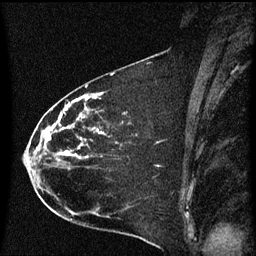
Breast MRI (dynamic contrast-enhanced), one sagittal slice. Position 33 of 60 along the scan axis. Dynamic contrast-enhanced series, image 2 of 3 at this slice position (ordered by acquisition). 1.5 T. TE 4.2 ms, TR 8.4 ms. 2 mm slice thickness. 256 × 256 image matrix, field of view 200 × 200 mm. Patient: female, 35 years. From the clinical record (not read from this slice): setting: breast cancer imaged before/during neoadjuvant chemotherapy; receptor status: HER2-positive.
Structures marked on this image (semi-automatic segmentation, software-assisted and operator-edited):
- analysis volume of interest (the breast-tissue region the enhancement analysis was run in; not a lesion): bounding box (x1, y1, x2, y2) in pixels: (25, 68, 173, 173)
- tumour enhancement mask (voxels above the 70 % enhancement threshold inside the analysis volume of interest): (33, 96, 99, 165)